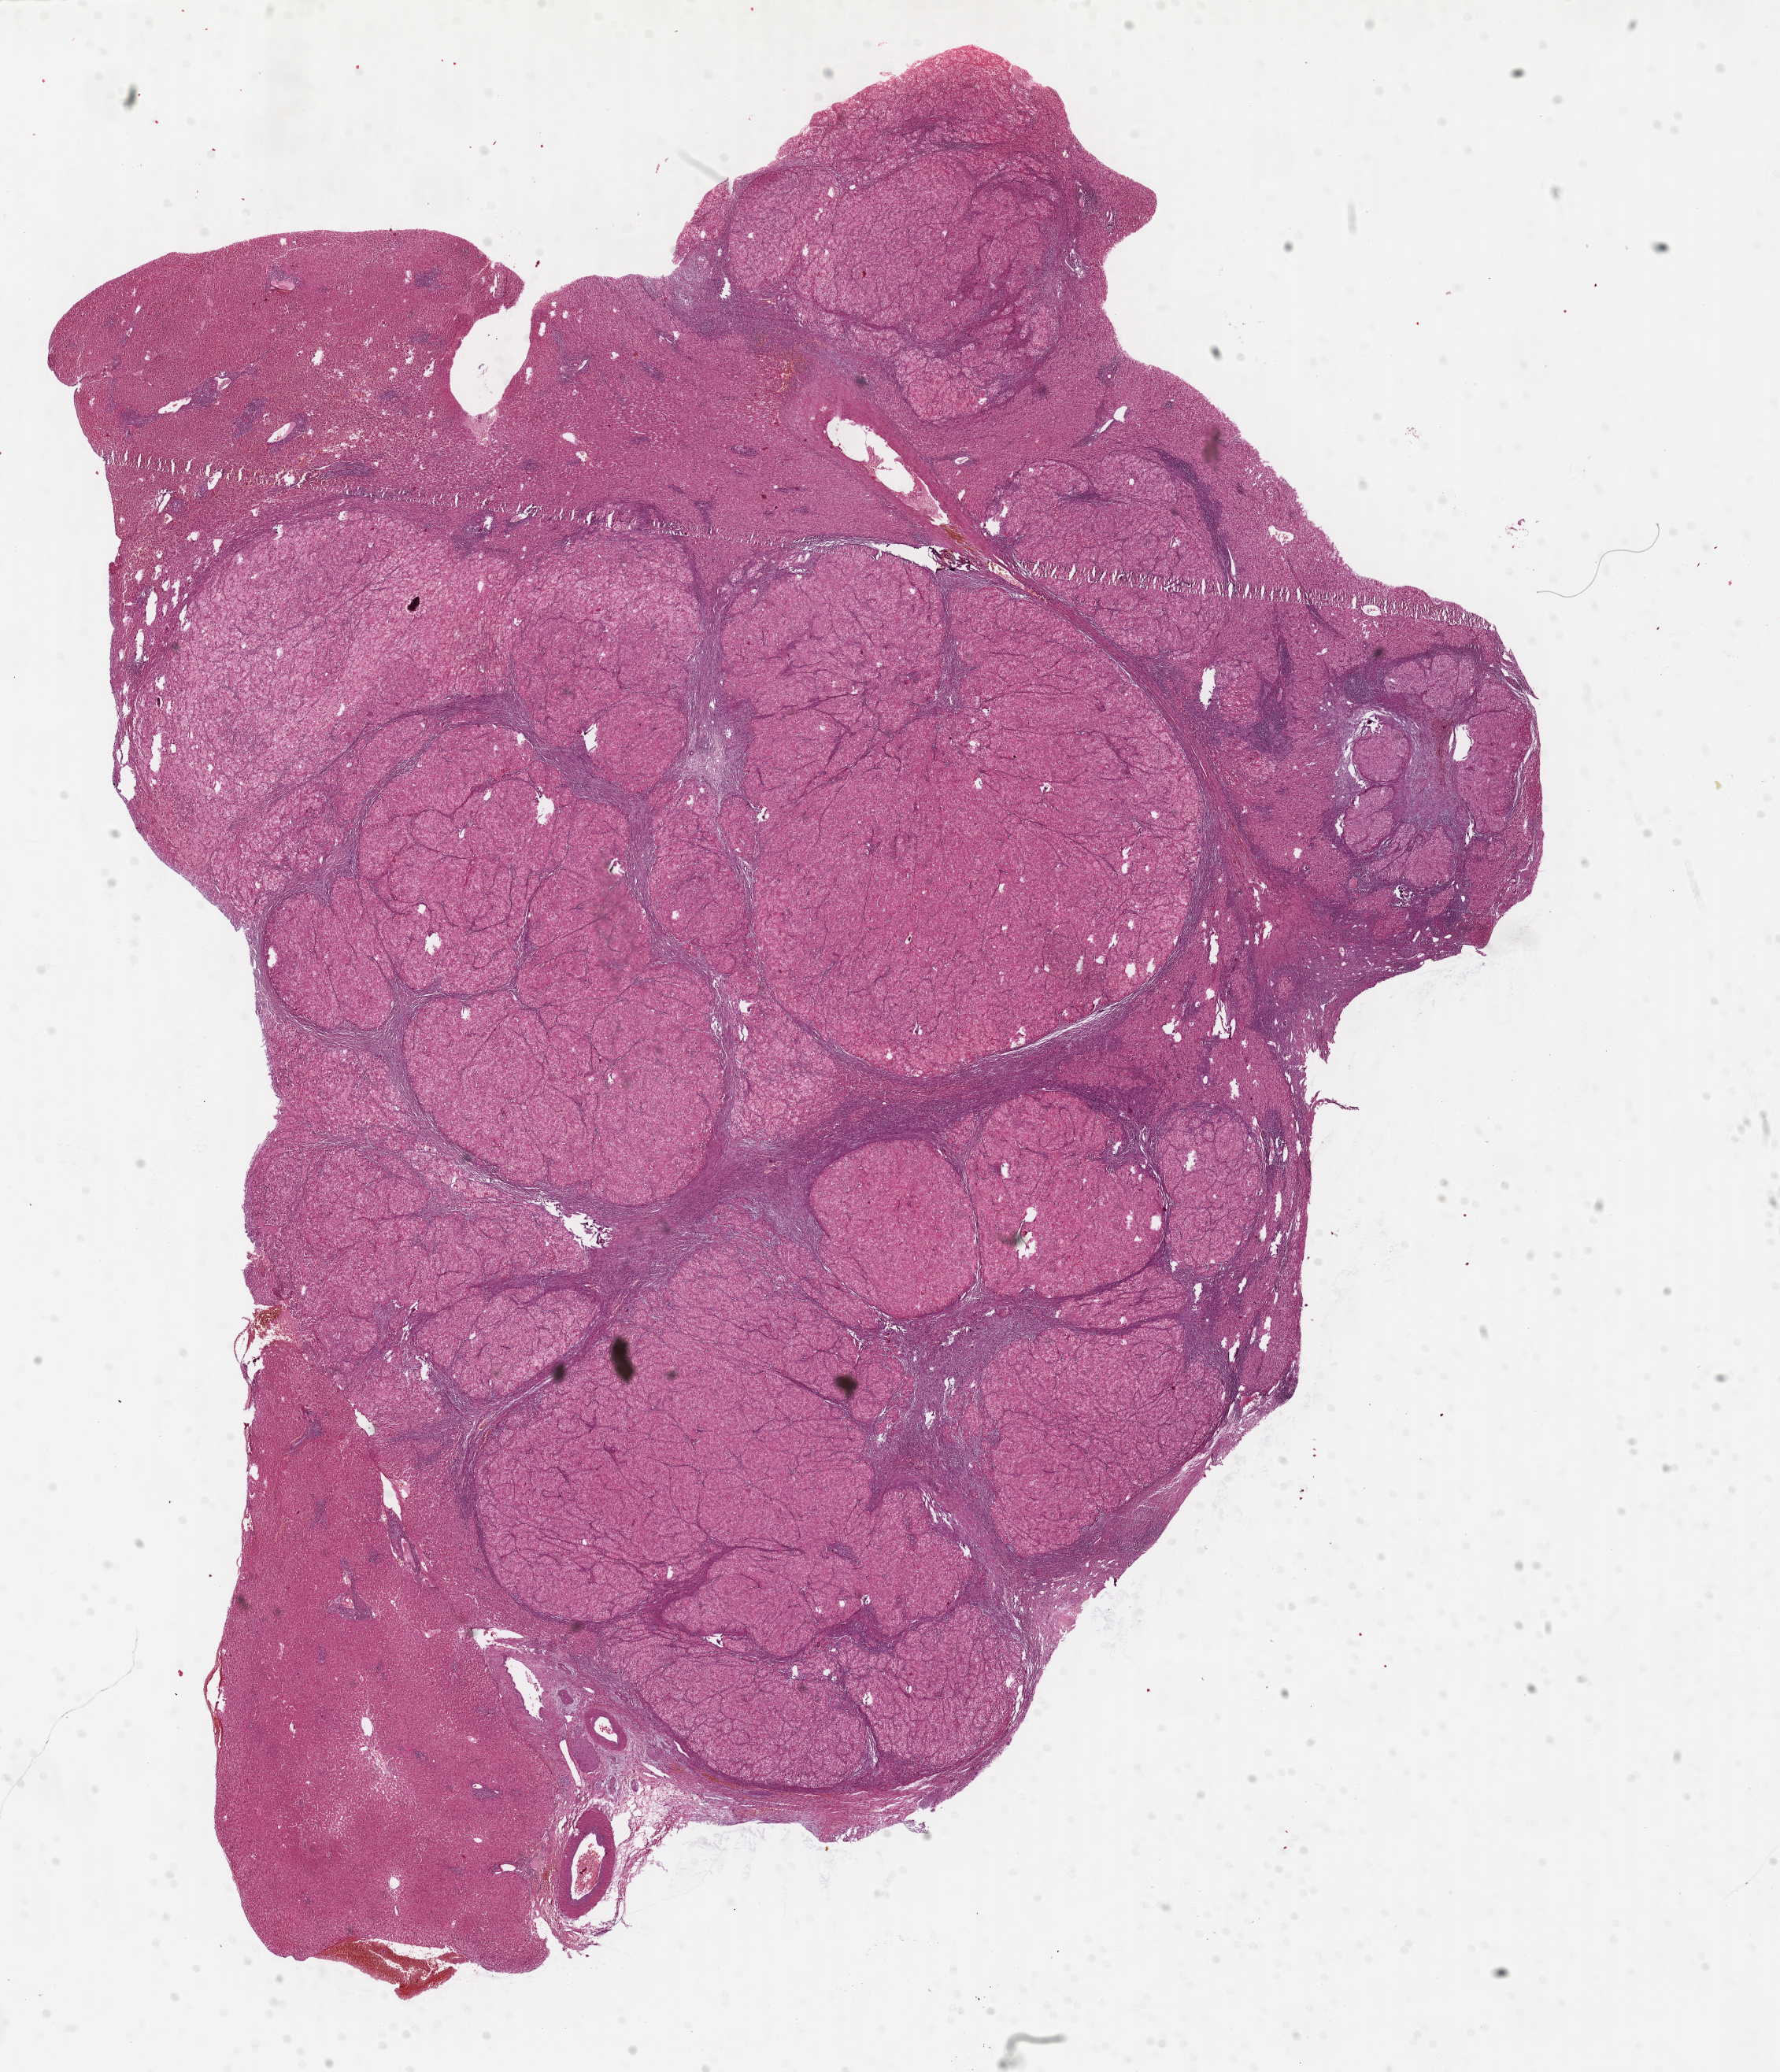
H&E-stained whole-slide image — shown as a low-resolution overview of the whole scanned area (about 17.8 x 20.7 mm). Formalin-fixed paraffin-embedded (FFPE) diagnostic section. Sample: primary tumour, liver. Male patient; age at initial diagnosis 48 years.
Histologic diagnosis: Hepatocellular carcinoma, NOS.